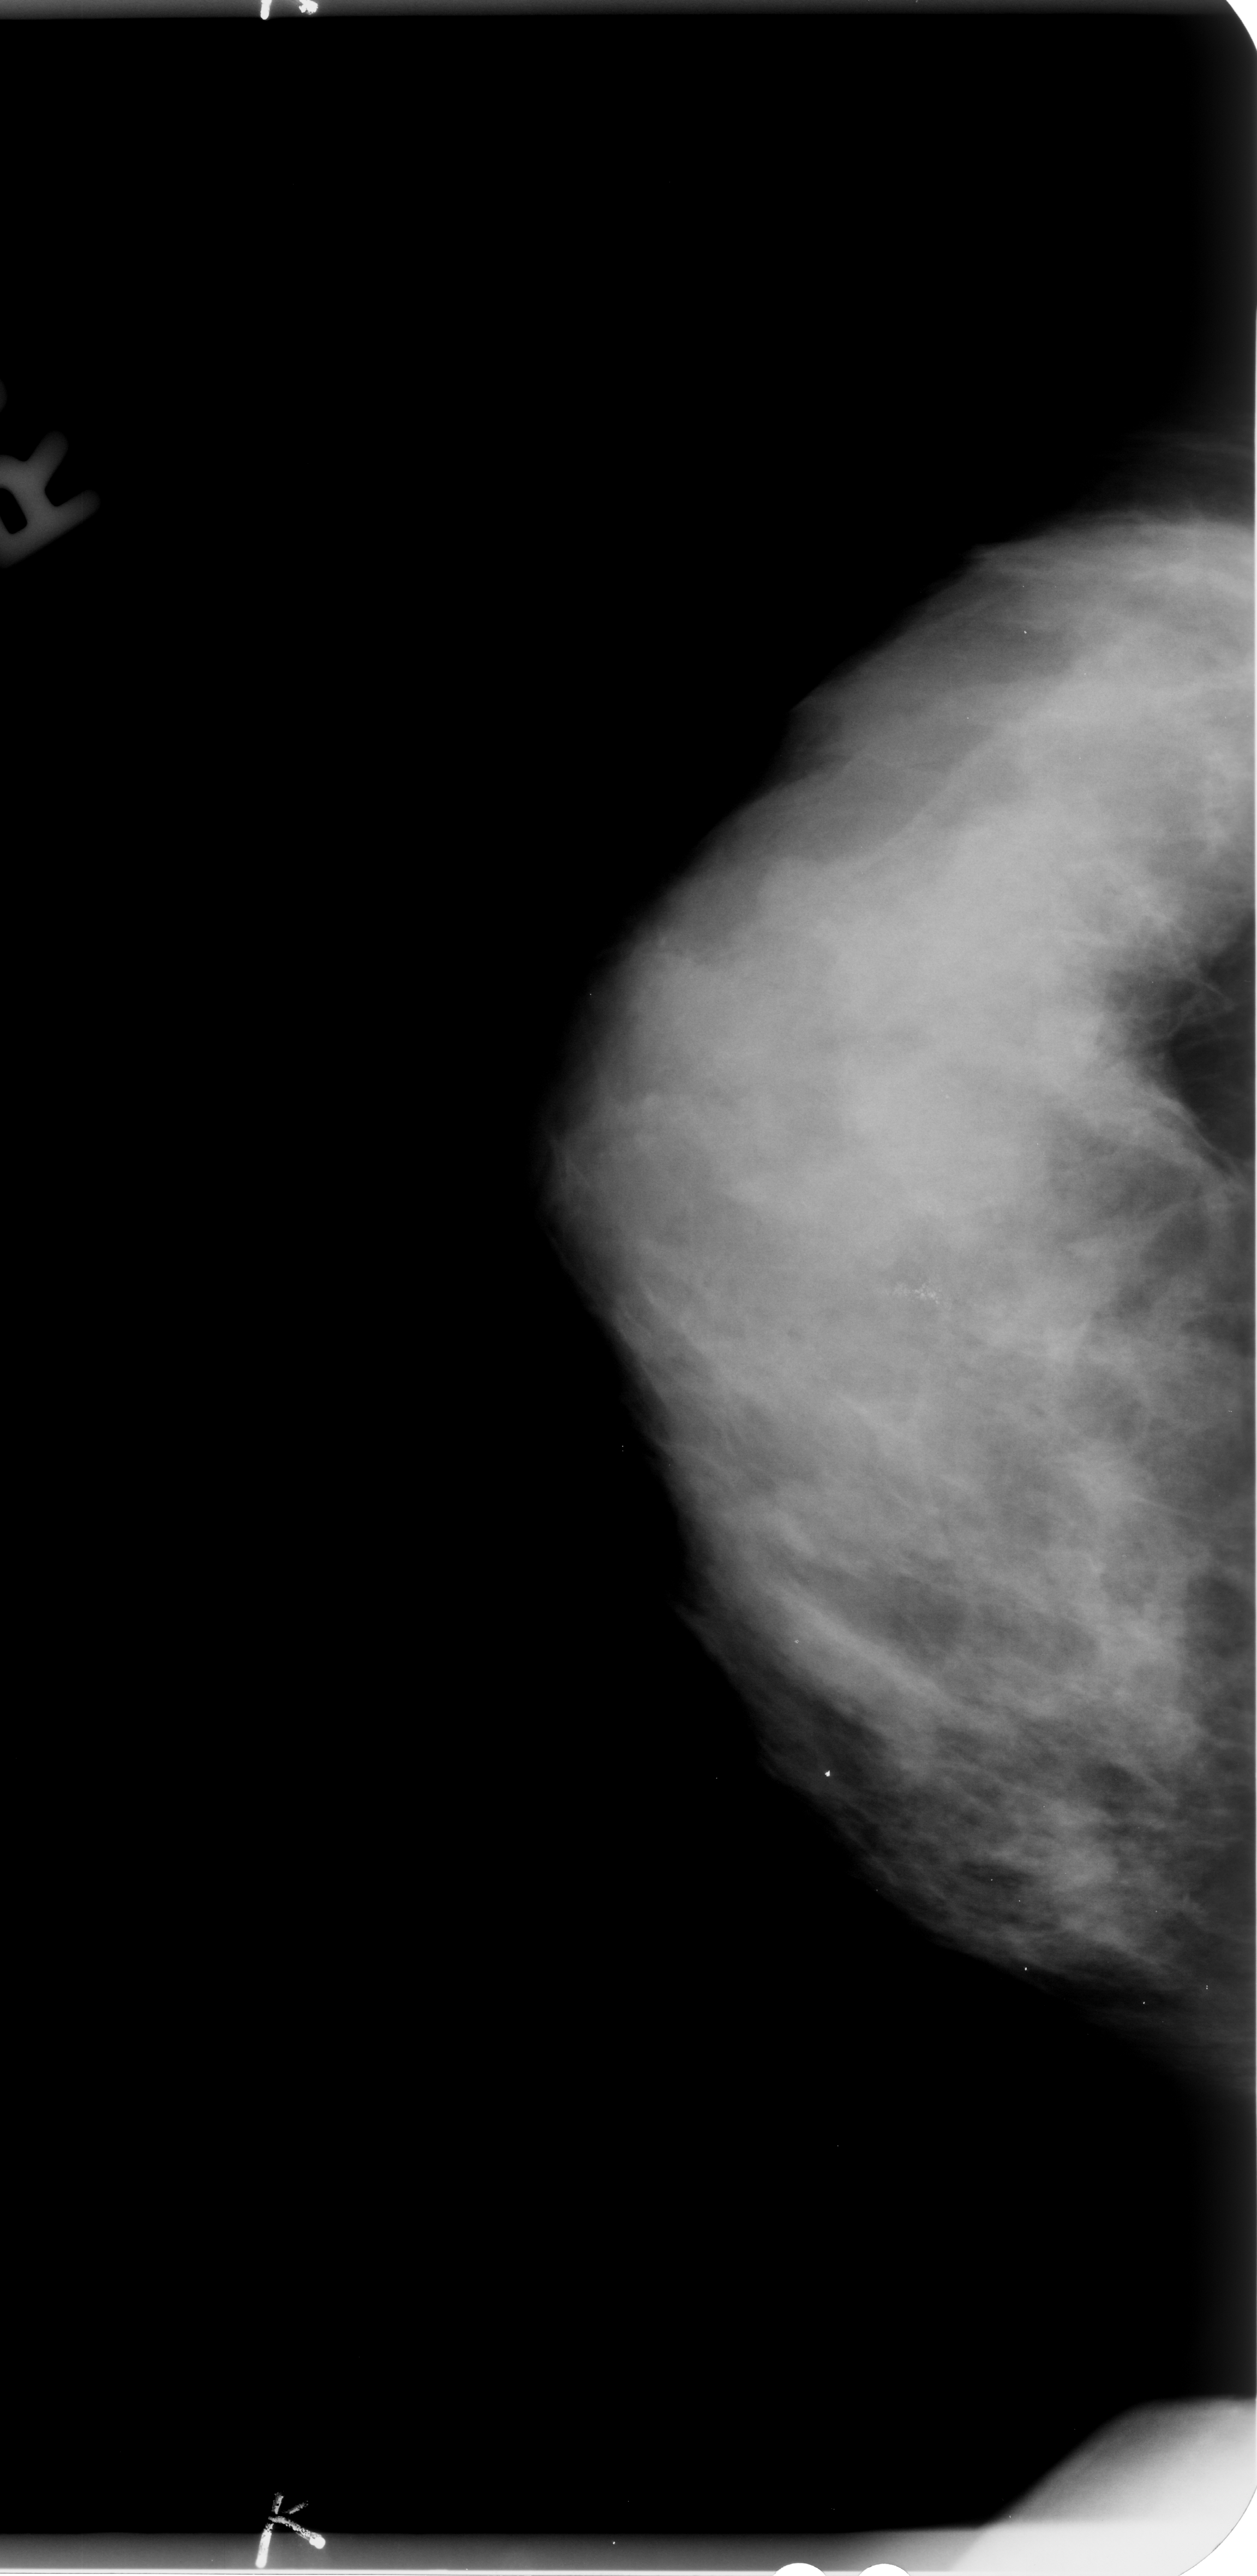
Mammogram (digitized film), right breast, CC view, breast composition: extremely dense (BI-RADS density category 4 of 4).
- Marked findings (only marked abnormalities are described; nothing is implied about the rest of the image): calcifications, morphology pleomorphic, distribution clustered; BI-RADS assessment category 4; pathology (as recorded): benign.